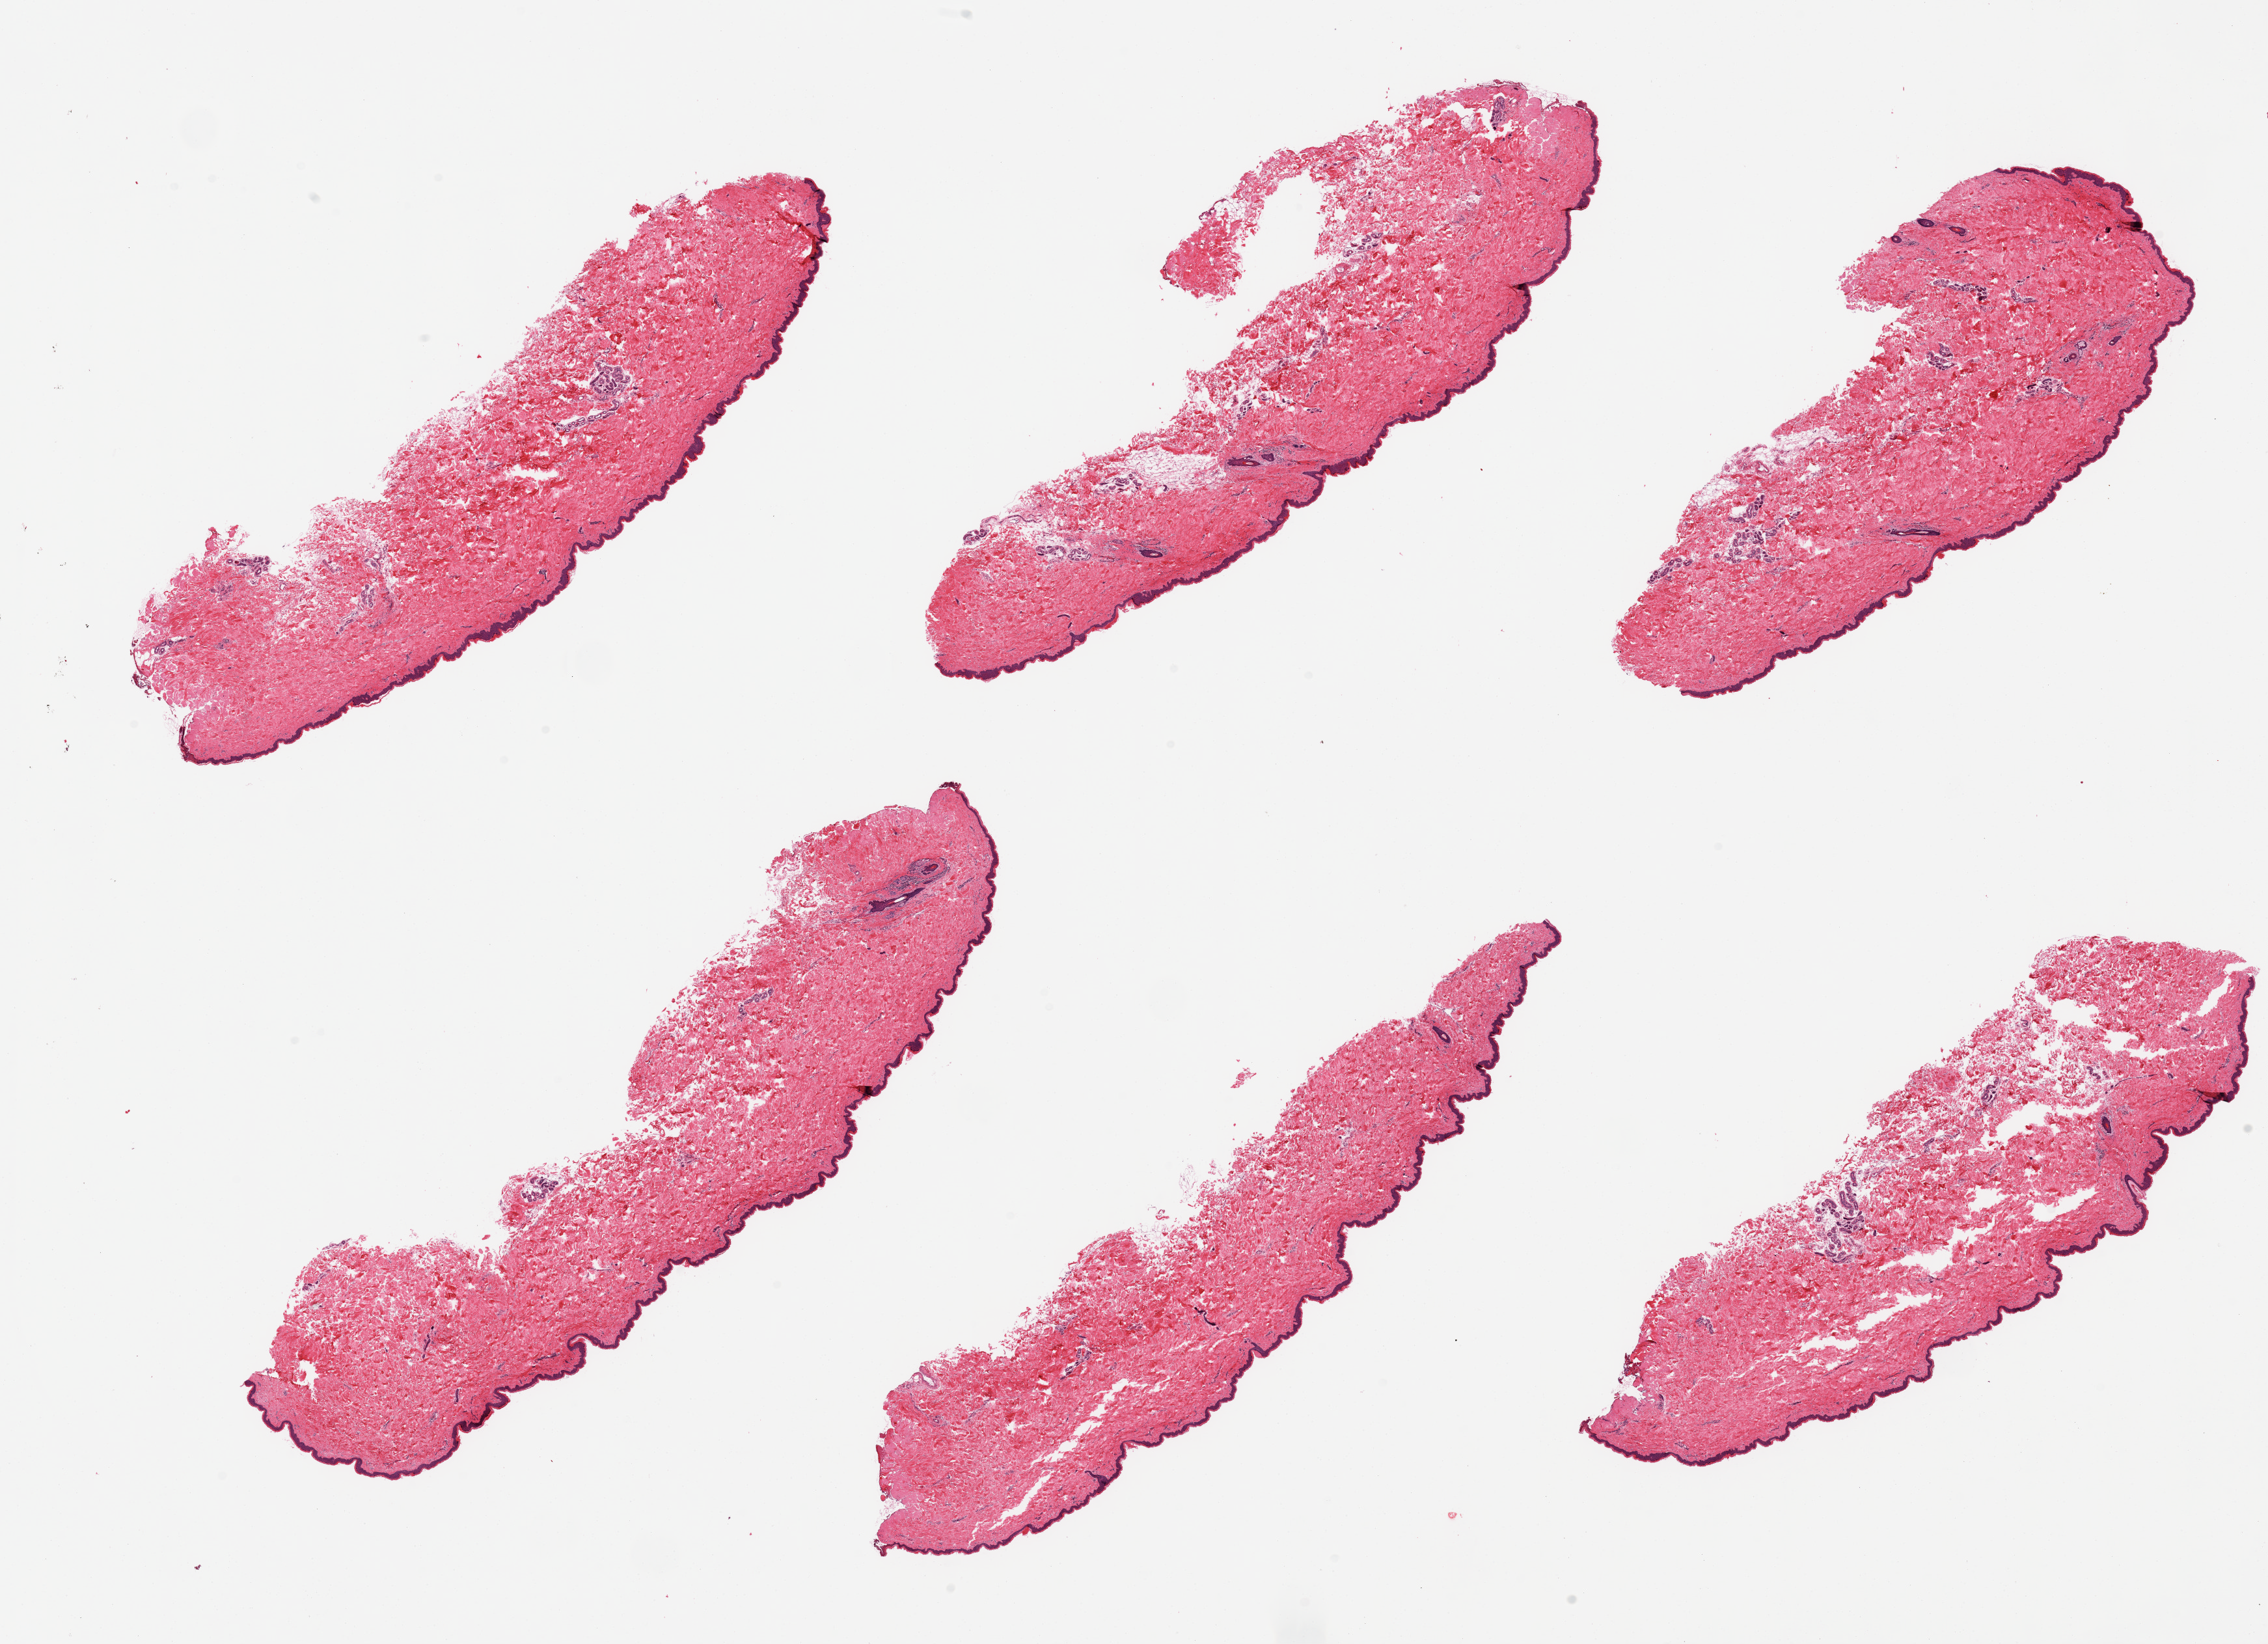
Hematoxylin and eosin (H&E) whole-slide image, shown as a low-resolution overview of the whole scanned area (about 27.6 x 20.0 mm, slide scanned at 20x); PAXgene-fixed paraffin-embedded (PFPE) section; section of skin of suprapubic region (target tissue); donor tissue sample. Female donor.
Review note (as recorded): 6 pieces, minimal dermal fat.